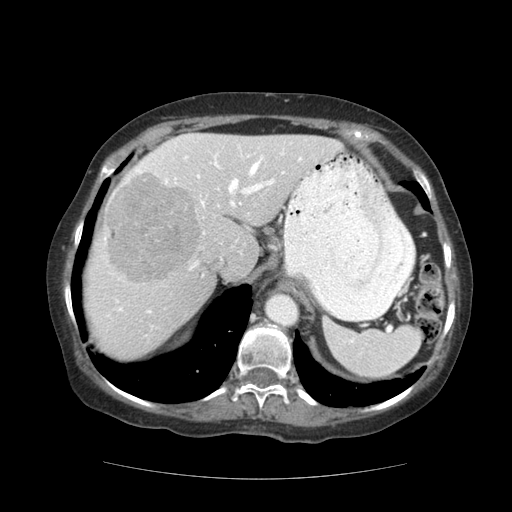
Contrast-enhanced abdominal CT (liver protocol), one axial slice; slice 86 of 111 in the series (ordered by position); reconstruction kernel STANDARD; soft-tissue window (W 400 / L 40 HU); 2.5 mm slice thickness; 512 × 512 image matrix, field of view 360 × 360 mm. From the clinical record (not read from this slice): diagnosis: hepatocellular carcinoma (patient treated with transarterial chemoembolisation; whether this scan precedes or follows treatment is not stated here); TNM stage (as recorded): Stage-I; Child-Pugh class: A; tumour nodularity: uninodular; tumour size: 7.3 cm.
Annotated regions visible in this slice (semi-automatically segmented with operator editing):
- liver parenchyma outside the tumour (the mass and vessels are separate outlines, so this box may not span the whole liver): bounding box (x1, y1, x2, y2) in pixels: (84, 134, 342, 360)
- mass: (106, 171, 202, 283)
- liver vessels: (104, 136, 302, 316)